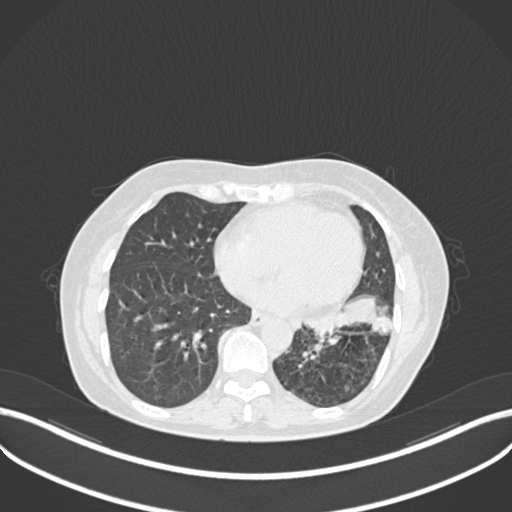
Chest CT, one axial slice; slice 96 of 270 in the series (ordered by position); reconstruction kernel B30f; 120 kVp; lung window (W 1500 / L -600 HU); 1 mm slice thickness; 512 × 512 image matrix, field of view 400 × 400 mm. Patient: female, 63 years. From the clinical record (not read from this slice): clinical TNM (as recorded): T1b N0 M0.
Structures marked on this image (bounding box drawn by a radiologist):
- lung tumour (recorded histology: adenocarcinoma): bounding box [x1, y1, x2, y2] px = [302, 291, 396, 340]